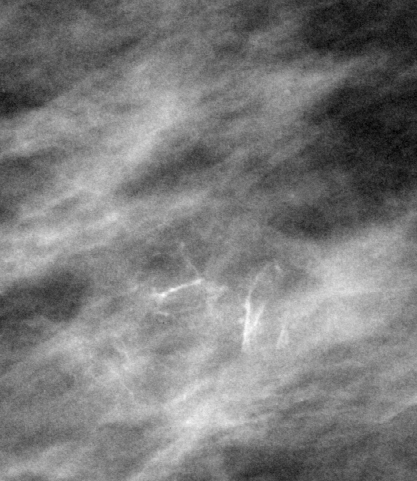
Crop from a digitized film mammogram around one marked abnormality; right breast; MLO view.
Finding: calcifications, morphology fine linear branching, distribution clustered; BI-RADS assessment category 4; subtlety rating 5 on a 1 (subtle) to 5 (obvious) scale; pathology (as recorded): benign.